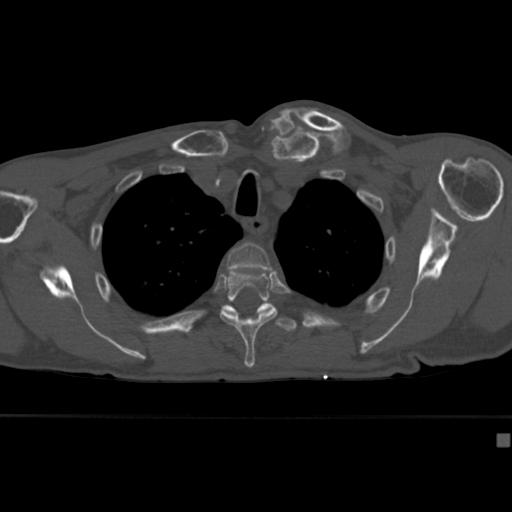
CT including the spine, one axial slice. Slice 321 of 430 in the series (ordered by position). Reconstruction kernel Br40s. Bone window (W 1800 / L 400 HU). 1.5 mm slice thickness. 512 × 512 image matrix. Male patient, age 64 years. Case-level facts recorded for this patient, not image findings: primary cancer: uterus; vertebrae with lytic lesions (as recorded): T1, T4, T5, T7, L5.
Outlined on this slice (semi-automatic segmentation, software-assisted and operator-edited):
- T3 vertebra: bounding box <227,242,273,271> (left, top, right, bottom; pixels)
- T4 vertebra: <220,271,284,369>
- T5 vertebra: <223,303,297,332>